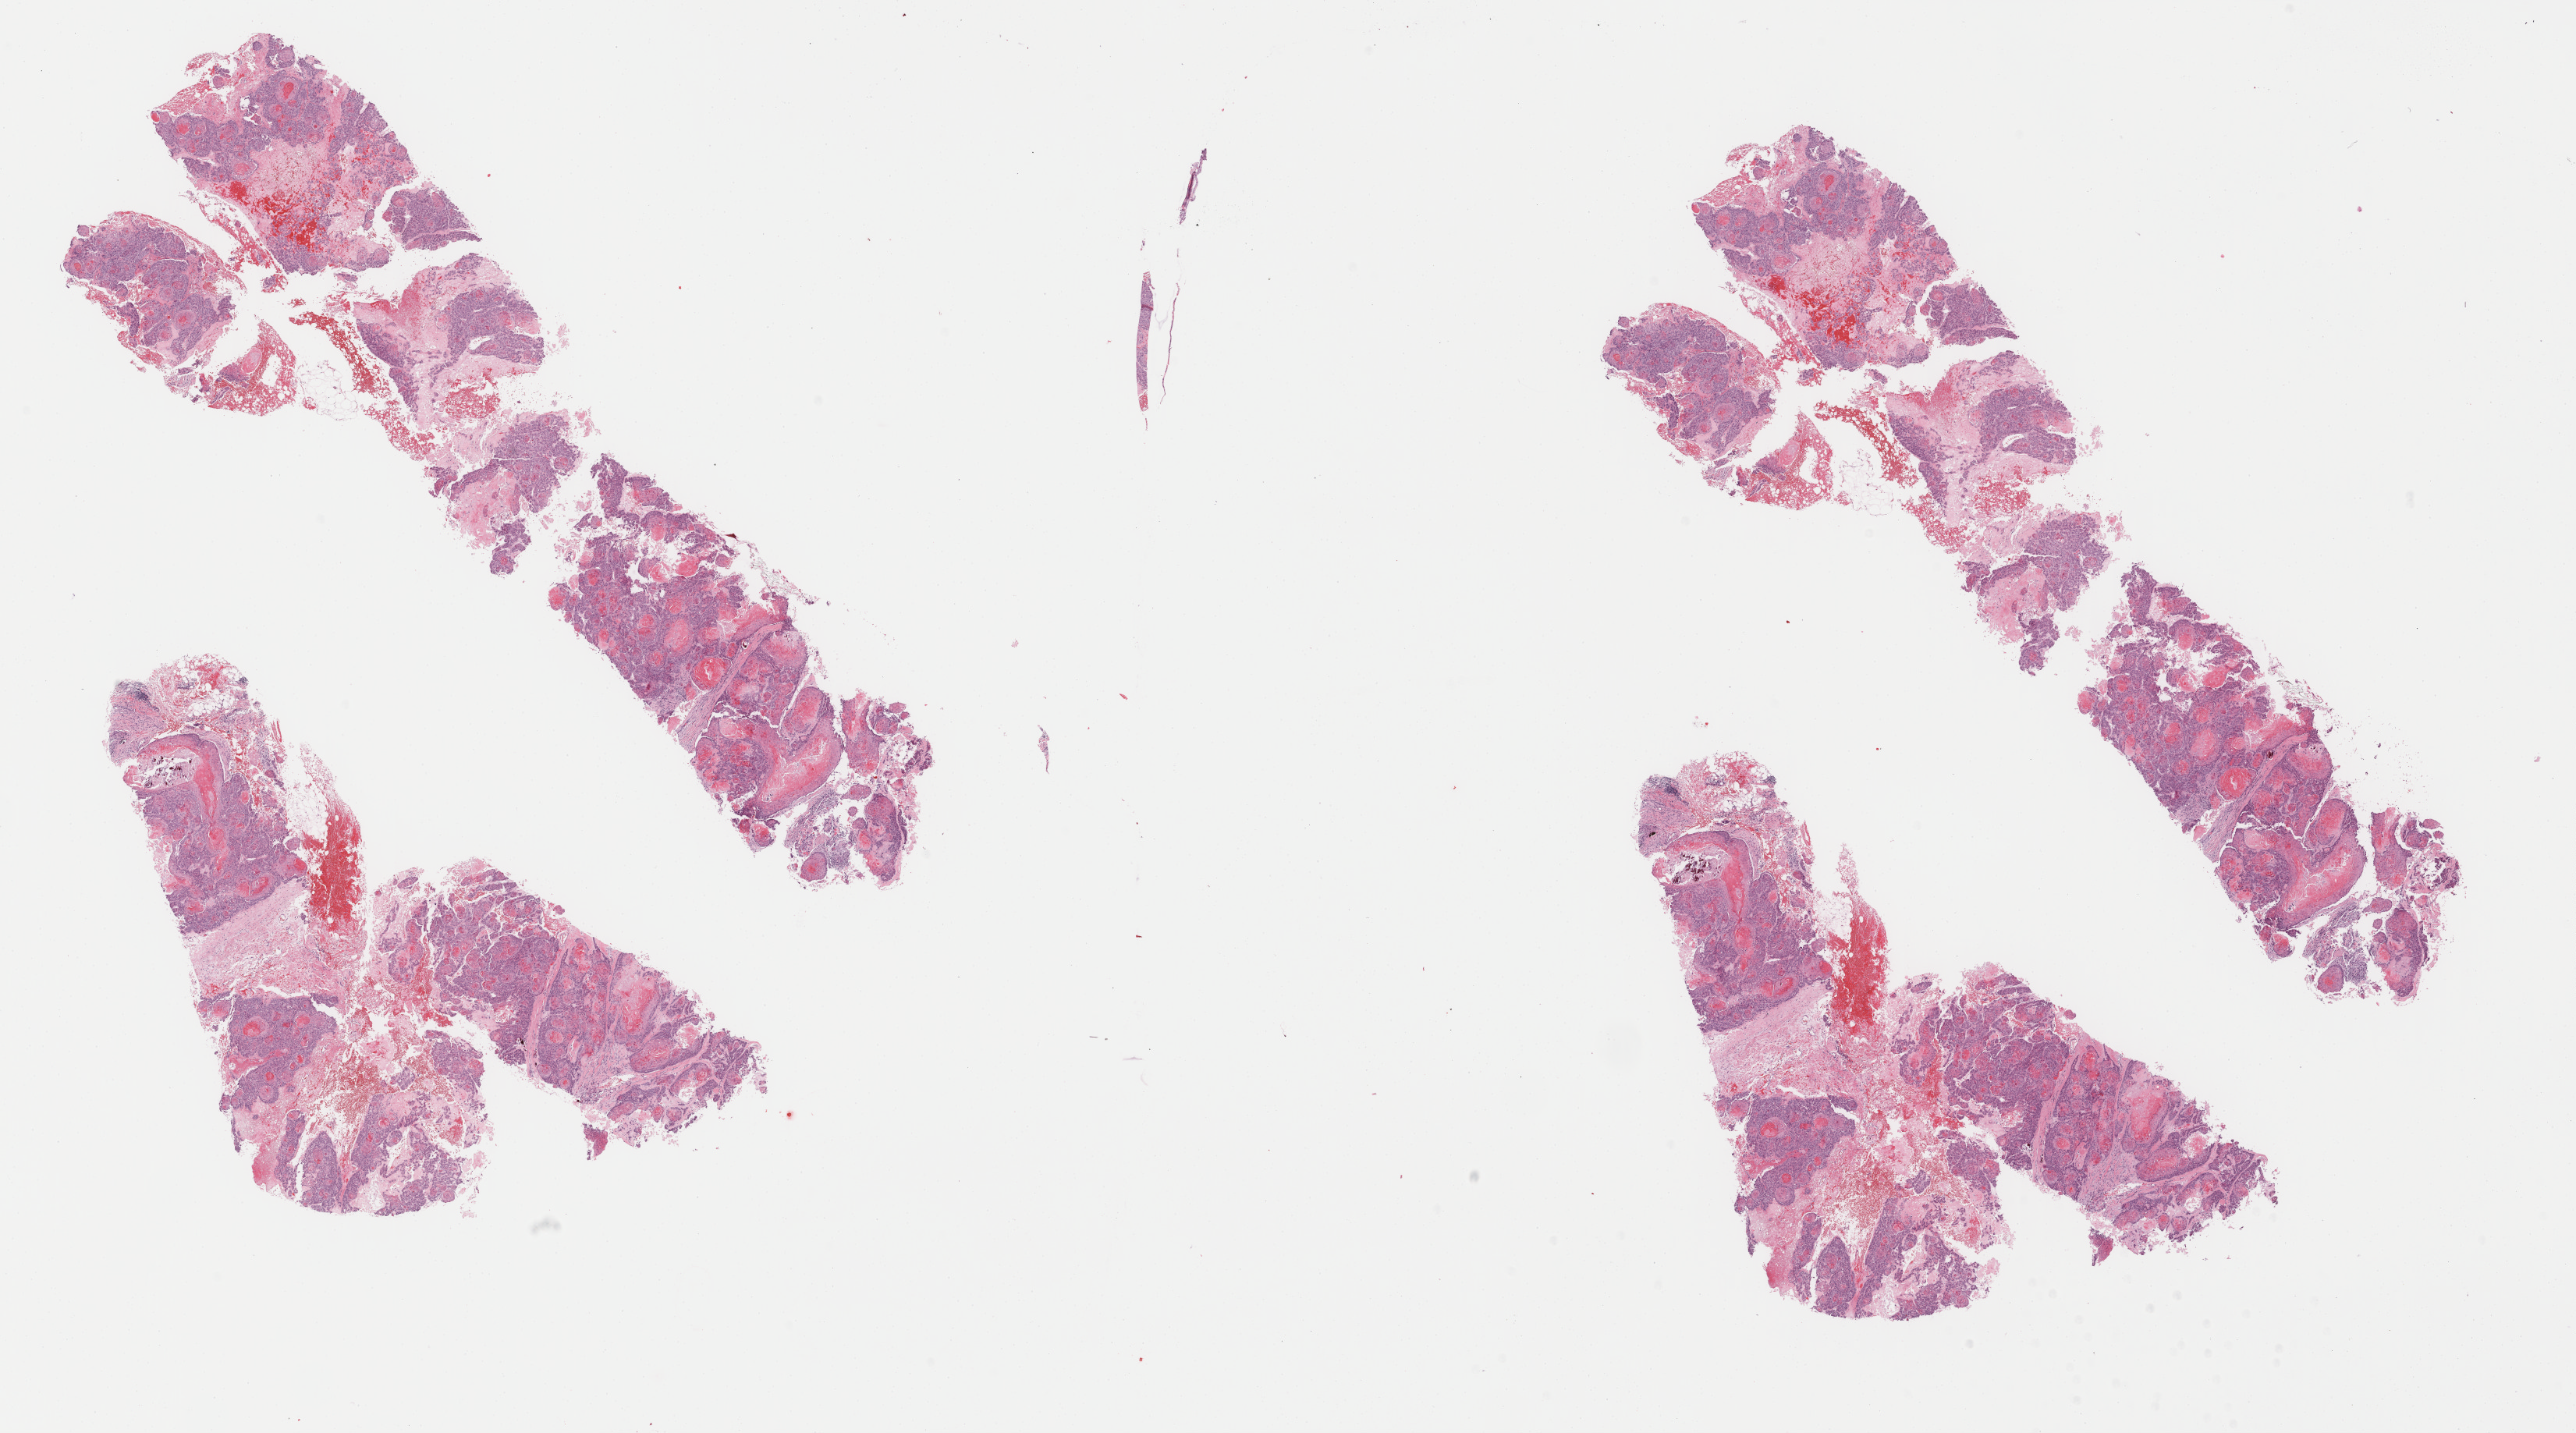
Whole-slide histology image, Hematoxylin and eosin (H&E) stained — a low-resolution overview of the entire scanned area, about 26.2 x 14.6 mm (from a 40x scan). Formalin-fixed paraffin-embedded (FFPE) diagnostic section. Sample: primary tumour, stomach. Patient: female, age at initial diagnosis 86 years. Histologic grade: G3 (poorly differentiated).
* AJCC pathologic stage: IIIA (7th edition)
* lymph nodes positive (case pathology): 6 of 44 examined
* diagnosis: Tubular adenocarcinoma (gastric antrum)